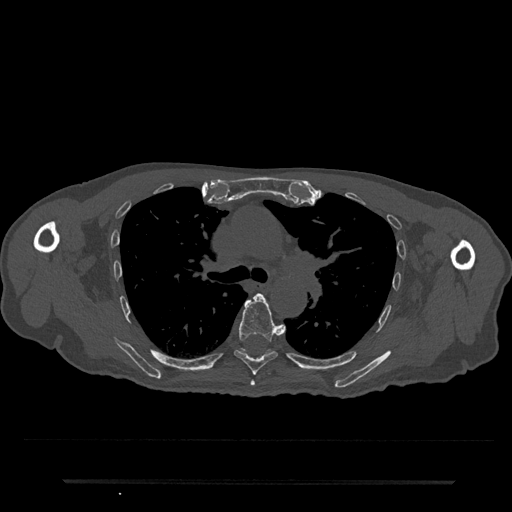
CT including the spine, one axial slice. Slice 527 of 797 in the series (ordered by position). 120 kVp. Bone window (W 1800 / L 400 HU). 512 × 512 image matrix. Male patient, age 74 years. Case-level facts recorded for this patient, not image findings: primary cancer: prostate.
Structures marked on this image (semi-automatically segmented with operator editing):
- T5 vertebra: bounding box <250,380,255,386> (left, top, right, bottom; pixels)
- T6 vertebra: <234,293,285,376>
- T7 vertebra: <242,349,245,351>